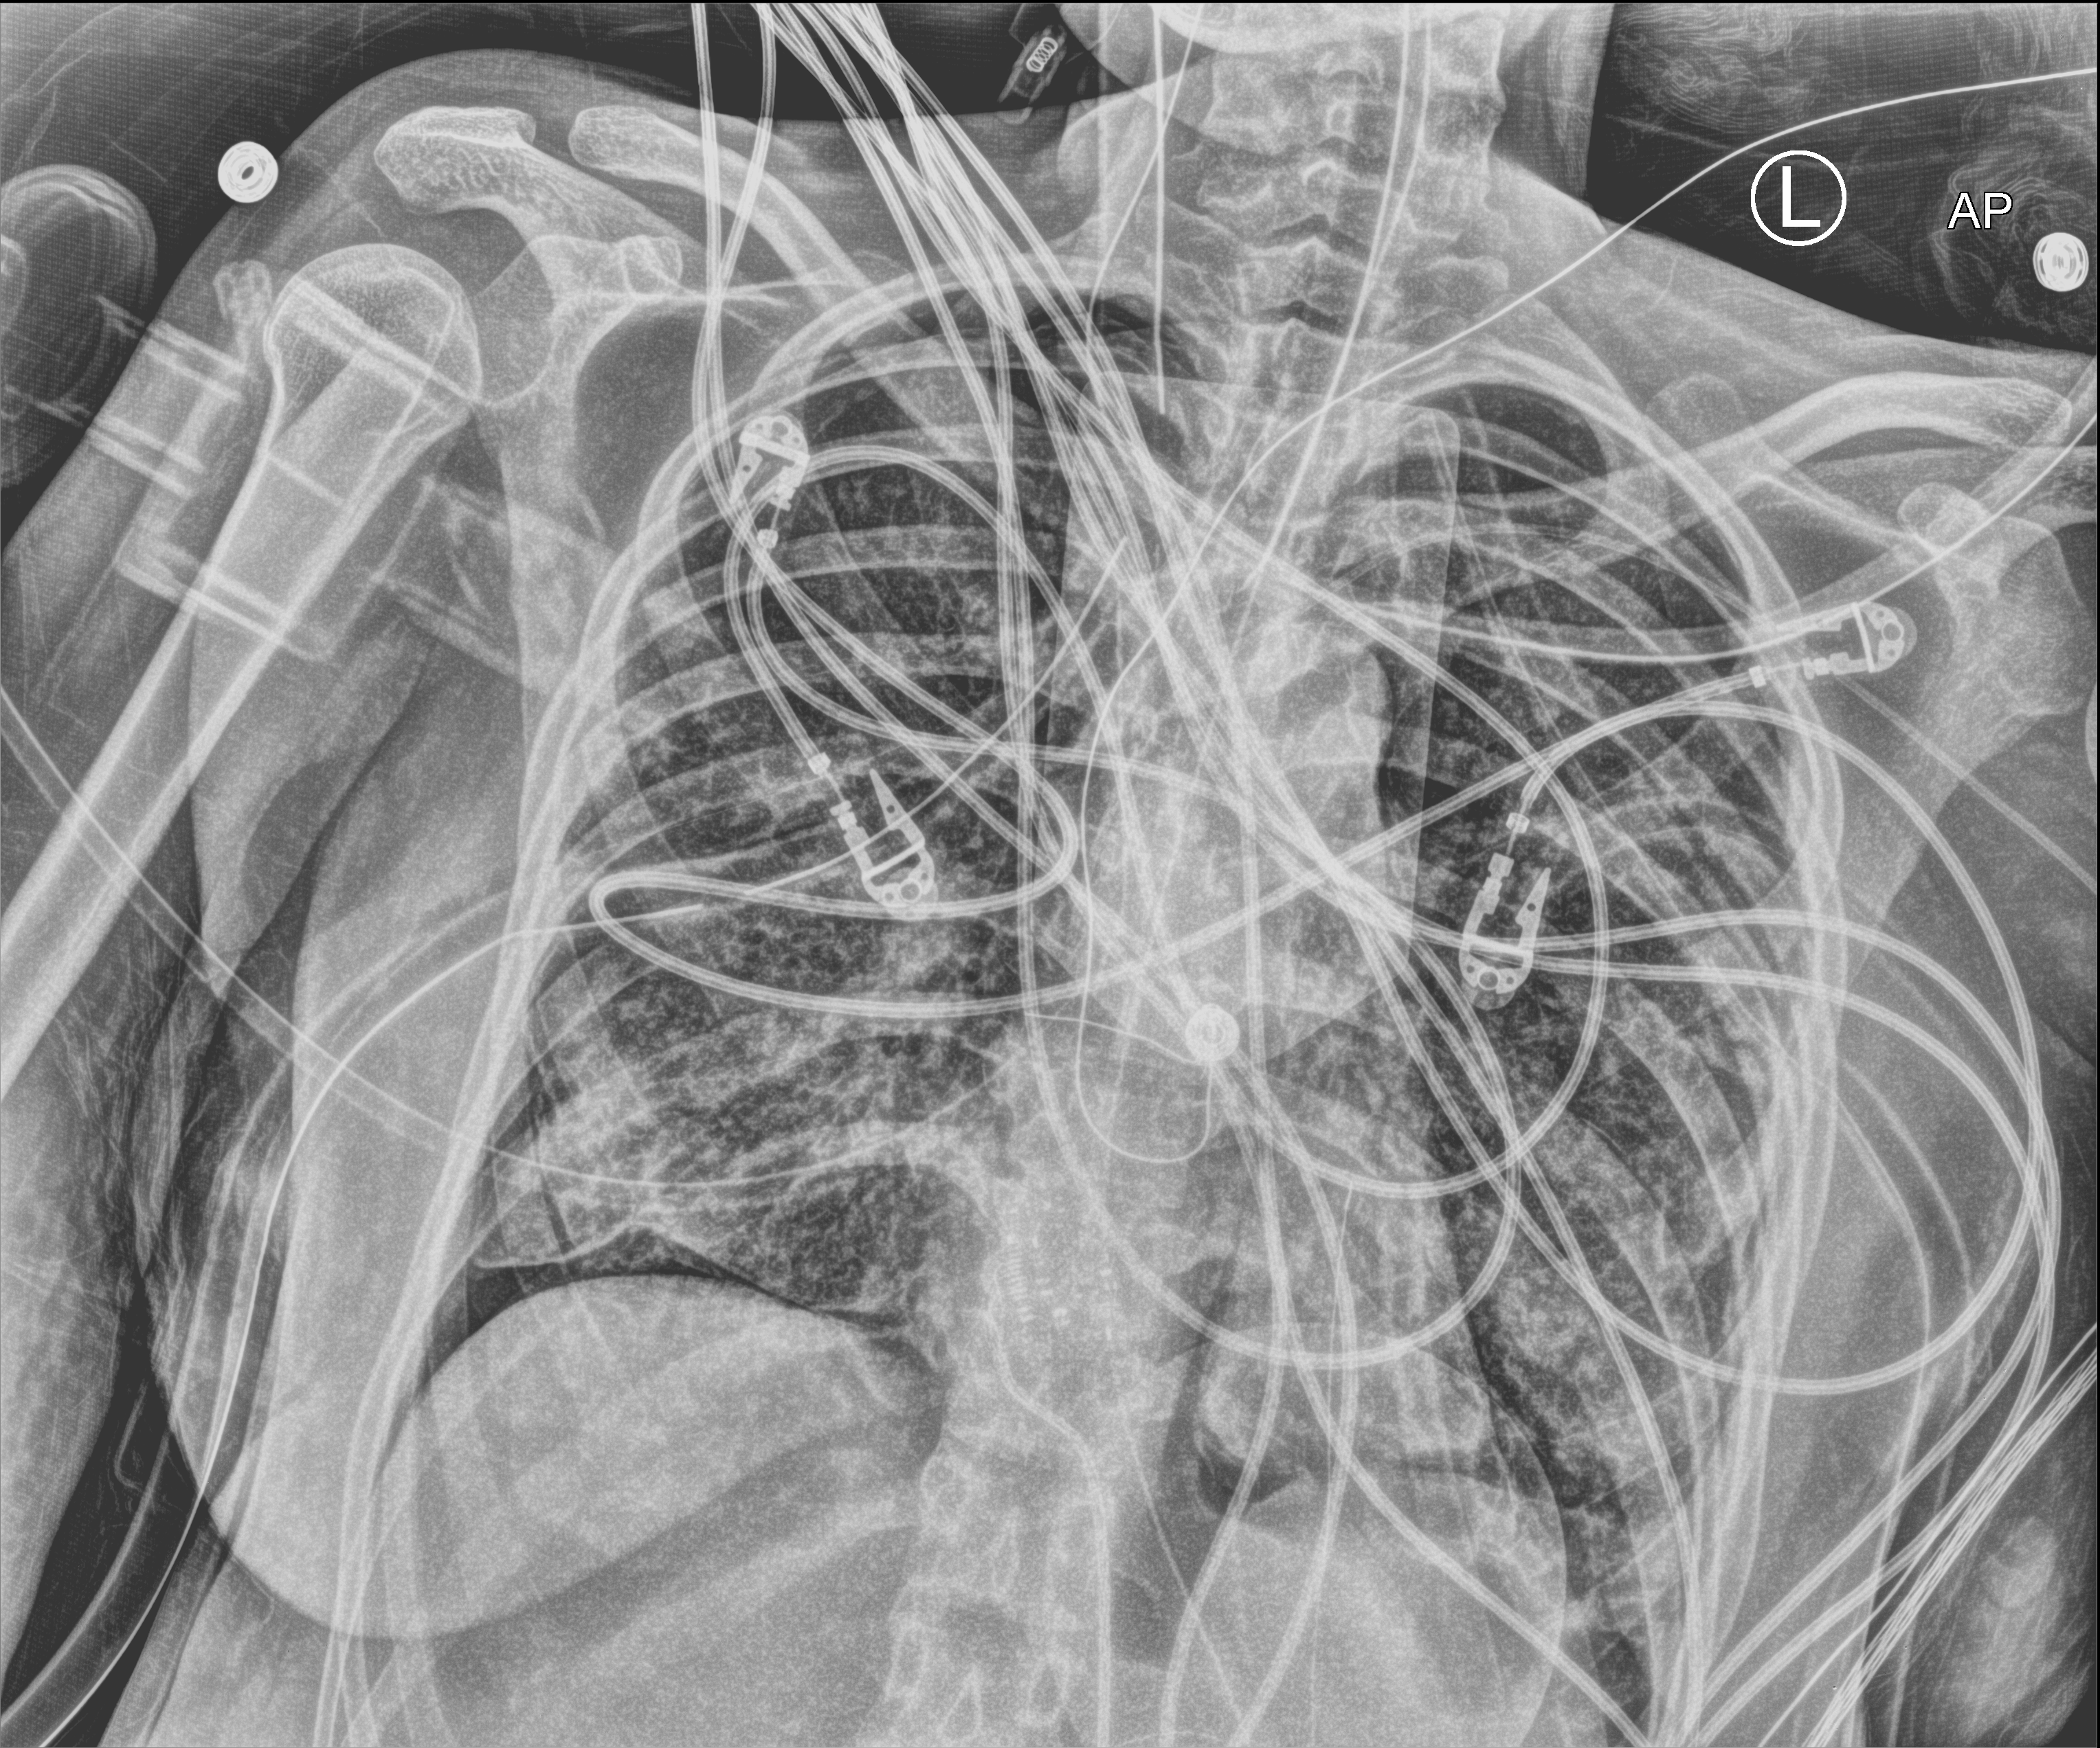
Portable chest radiograph. Adult patient hospitalised with COVID-19, age 18–59 years.
From the hospital-stay record, not from the radiograph (when in the stay this image was taken is not recorded): mechanically ventilated during this hospital stay: yes.